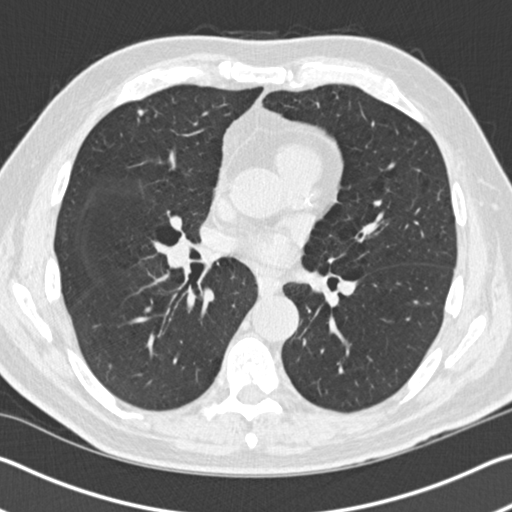
Axial slice from a low-dose chest CT screening exam. Baseline screening round. Lung window (W 1500 / L -600 HU). Standard (soft-tissue) reconstruction kernel (B30f). Slice 87 of 165 in the series. 512 × 512 image matrix. Male, age 69 years at enrolment.
Expert-annotated lung lesion, bounding box <121,97,162,138> (left, top, right, bottom; pixels). Screening reader's record for this exam: no non-calcified nodule ≥4 mm recorded. Official screen result: negative screen, significant abnormalities not suspicious for lung cancer.